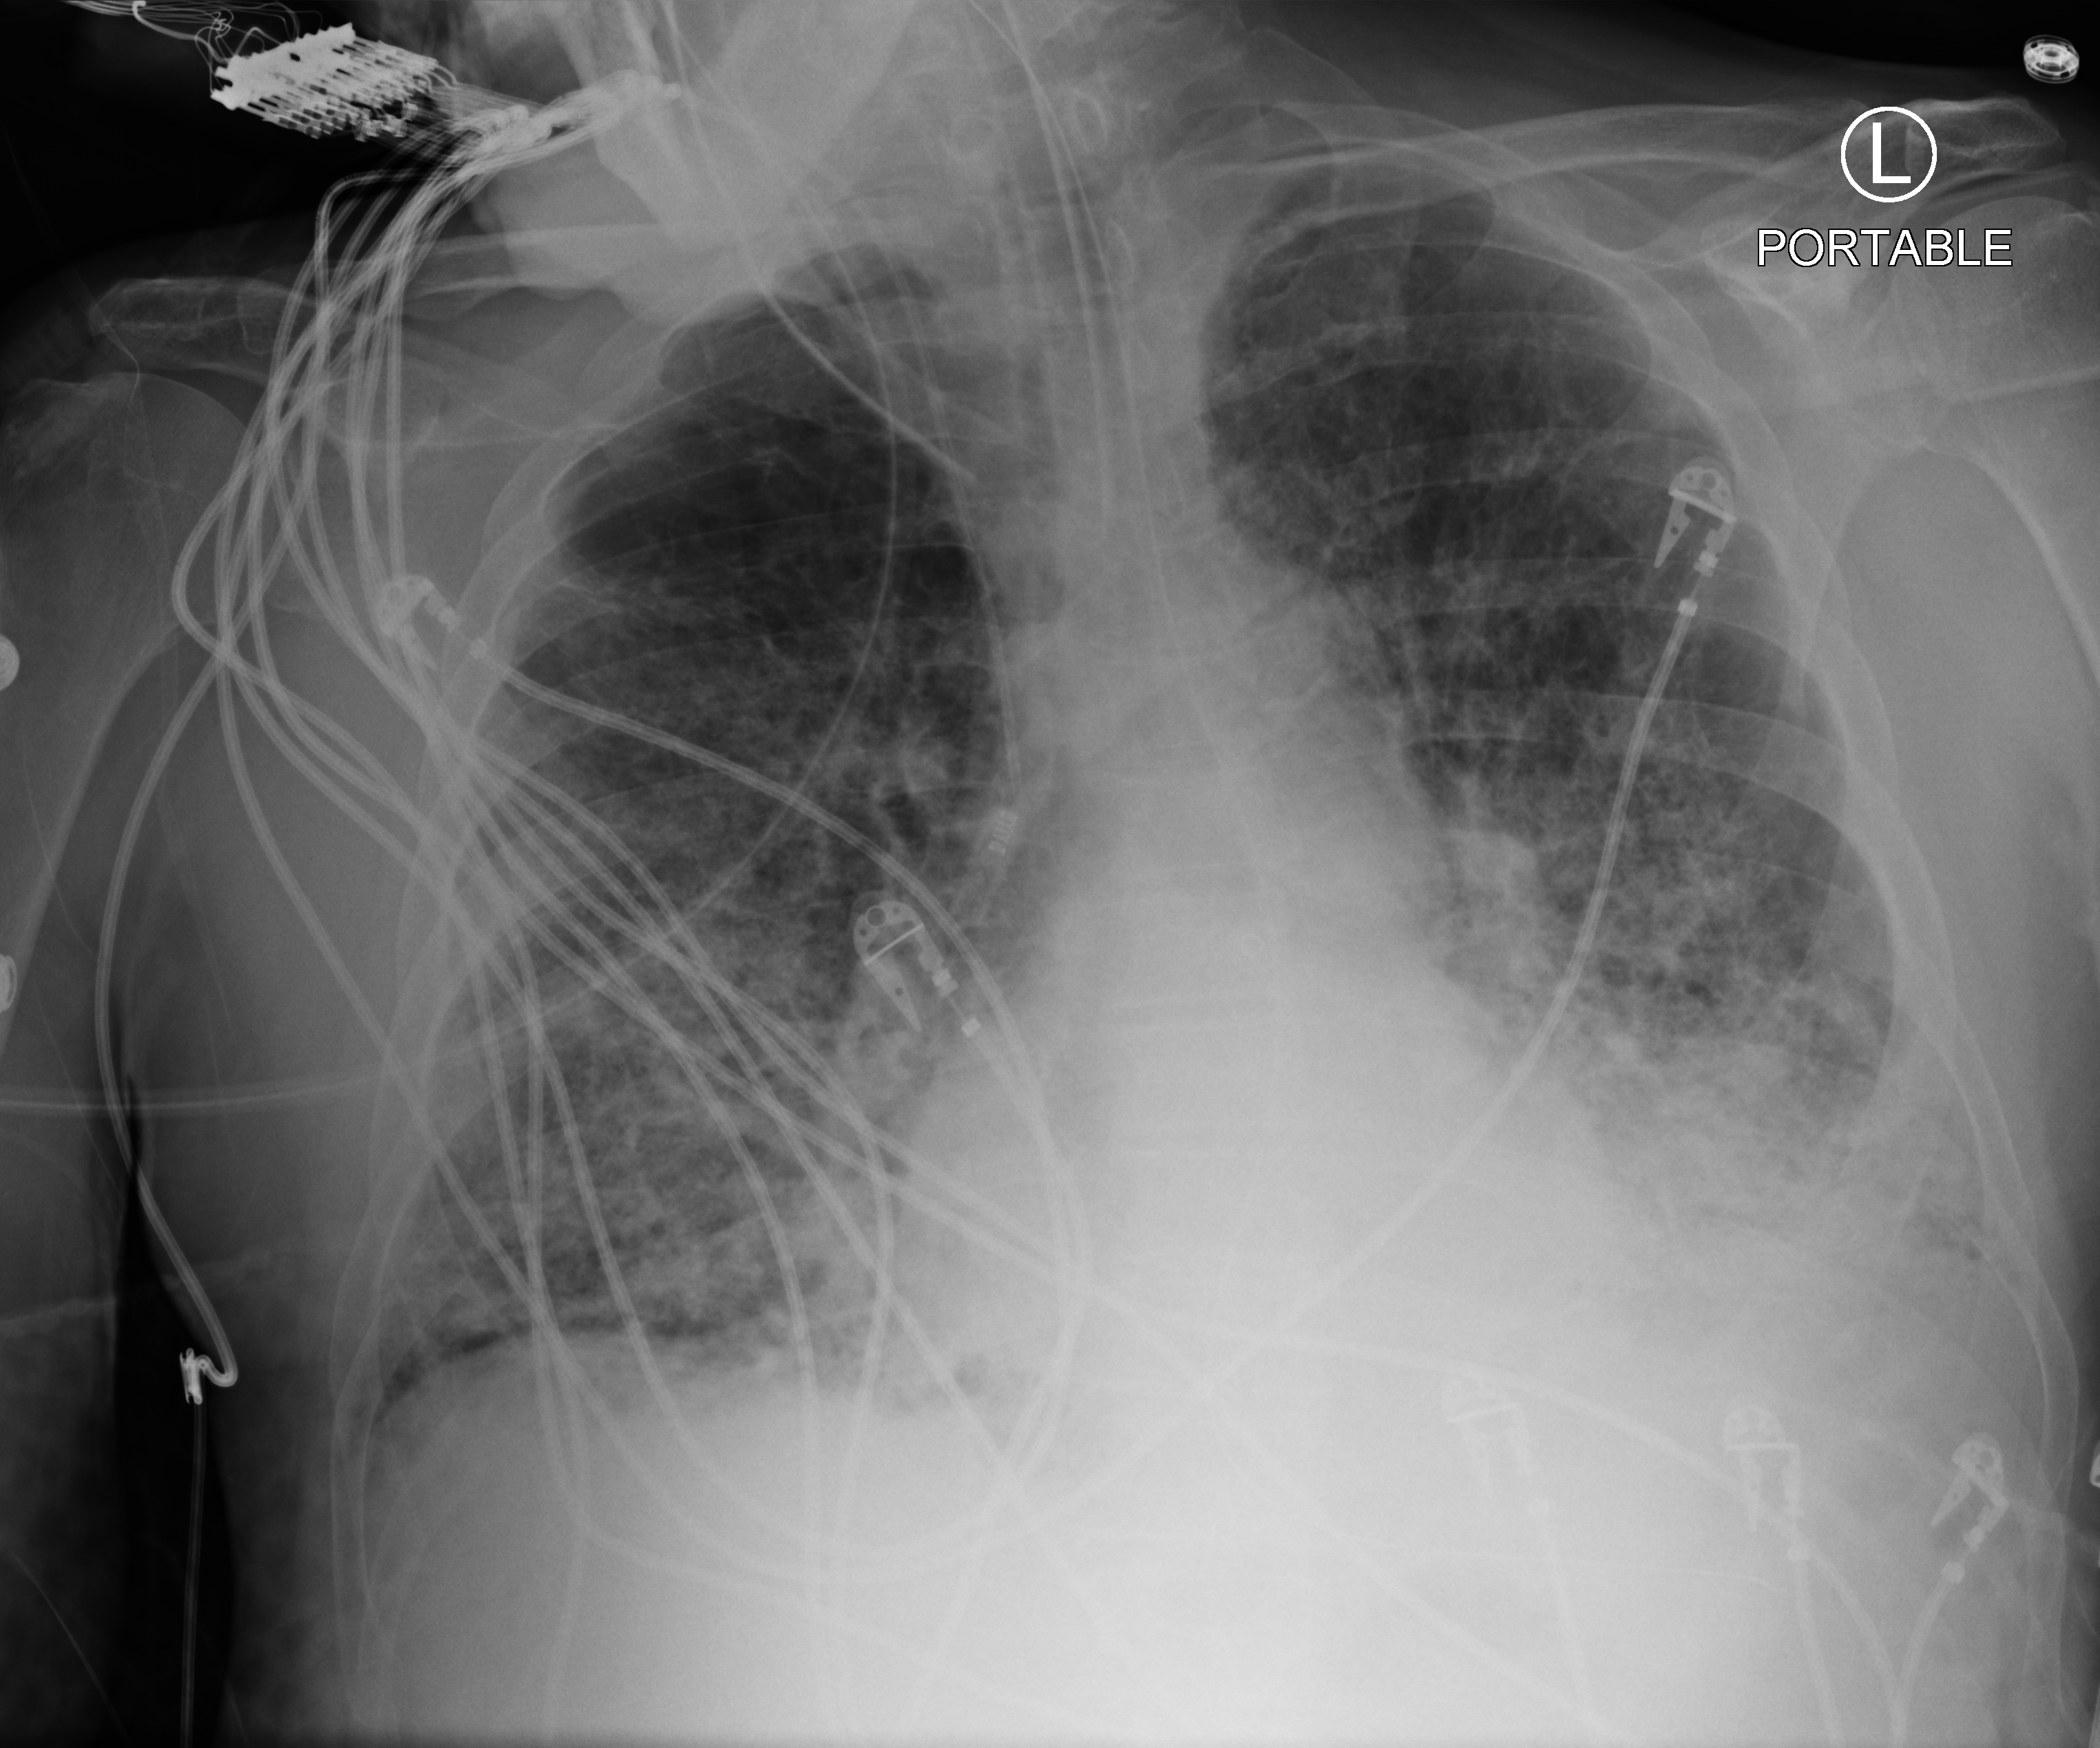
Bedside chest radiograph (computed radiography); anteroposterior (AP) projection. Patient hospitalised with COVID-19; male, aged 75–90 years.
From the hospital-stay record, not from the radiograph (when in the stay this image was taken is not recorded): hypertension (admission record): yes; mechanically ventilated during this hospital stay: yes; other chronic lung disease (admission record): yes.